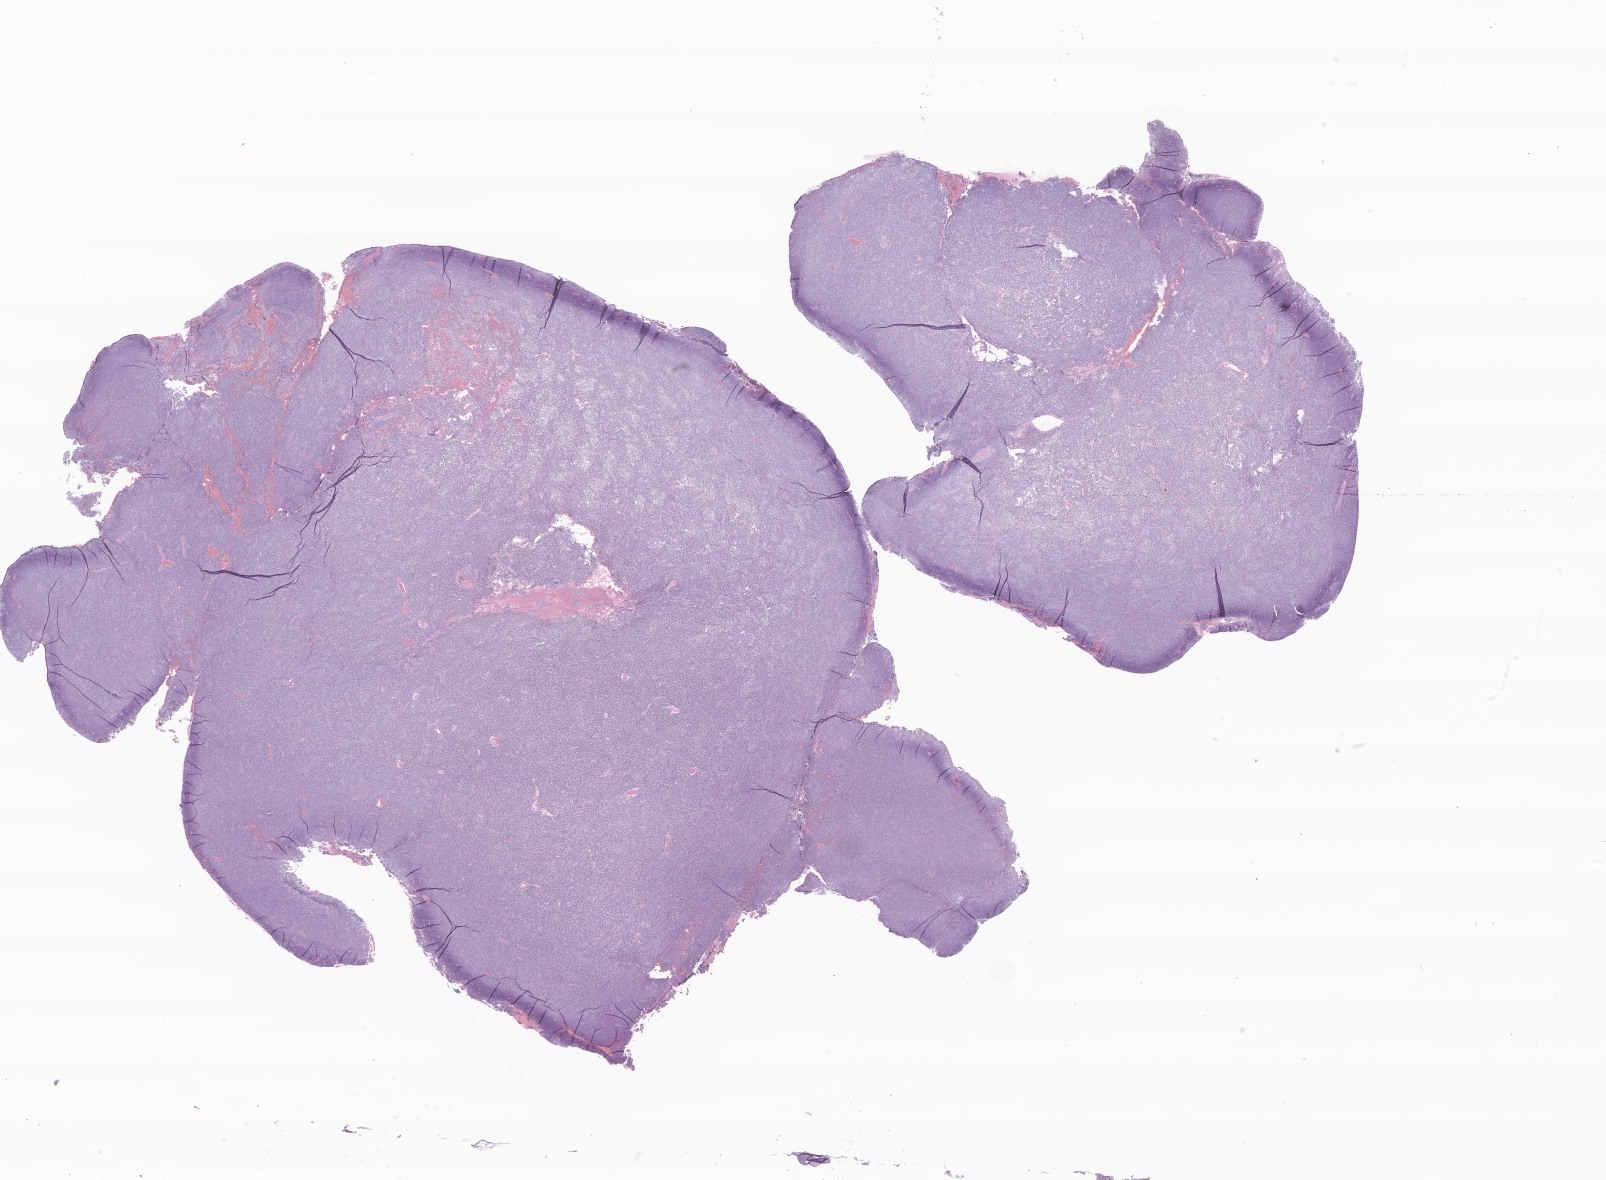
Haematoxylin and eosin whole-slide image of tumor tissue from the brain — low-resolution overview of the scanned area, about 27.1 x 19.9 mm, formalin-fixed paraffin-embedded section. Patient: male, age 293 months (24 years 5 months).
• diagnosis: Medulloblastoma, NOS